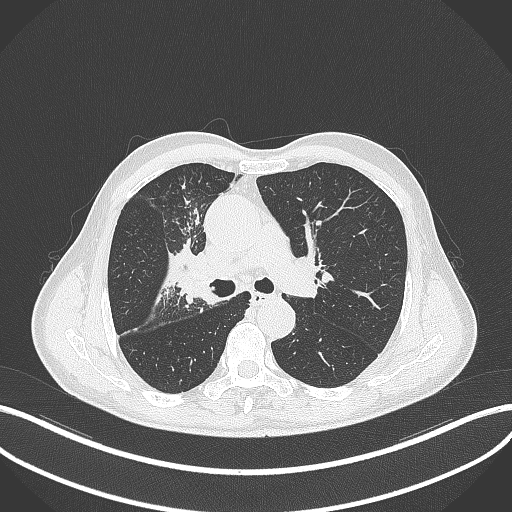
Chest CT, one axial slice; slice 307 of 490 in the series (ordered by position); reconstruction kernel B70f; lung window (W 1500 / L -600 HU); 1 mm slice thickness; 512 × 512 image matrix, field of view 400 × 400 mm. Patient: male, 69 years. From the clinical record (not read from this slice): clinical TNM (as recorded): T2a N0 M0.
Outlined on this slice (bounding box drawn by a radiologist):
- lung tumour (recorded histology: adenocarcinoma): box from (x=170, y=243) to (x=224, y=308) px